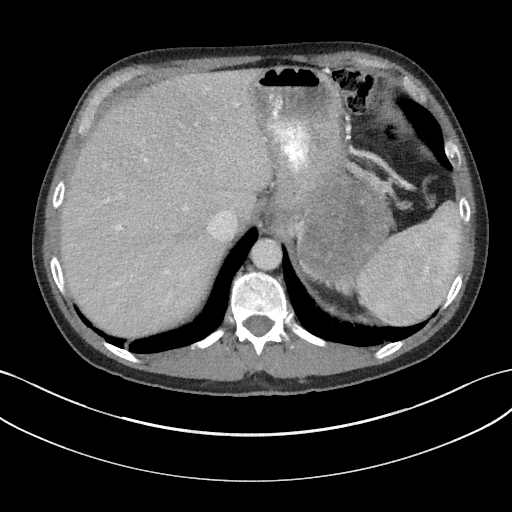
Contrast-enhanced abdominal CT, one axial slice; slice 128 of 147 in the series (ordered by position); reconstruction kernel I31f/3; intravenous contrast given; soft-tissue window (W 400 / L 40 HU); 3 mm slice thickness; 512 × 512 image matrix, field of view 384 × 384 mm. Patient: male, 58 years. Case-level facts recorded for this patient, not image findings: diagnosis: adrenocortical carcinoma; tumour side: left adrenal; tumour size at pathology: 22 cm; Ki-67 index: 26 %; stage (as recorded): 2.
Annotated regions visible in this slice (semi-automatic segmentation, software-assisted and operator-edited):
- mass: bounding box <301,181,388,278> (left, top, right, bottom; pixels)